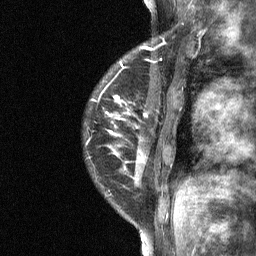
Breast MRI (dynamic contrast-enhanced), one sagittal slice. Slice 16 of 64 in the series (ordered by position). Dynamic contrast-enhanced study with each time point stored as its own series, time point 2 of 3 at this slice position (early post-contrast, ordered by acquisition time). 1.5 T. TE 4.8 ms, TR 27 ms. 2 mm slice thickness. 256 × 256 image matrix, field of view 180 × 180 mm. Patient: female, 34 years. From the clinical record (not read from this slice): setting: breast cancer imaged before/during neoadjuvant chemotherapy; receptor status: HR-positive, HER2-negative.
Outlined on this slice (semi-automatic segmentation, software-assisted and operator-edited):
- analysis volume of interest (the breast-tissue region the enhancement analysis was run in; not a lesion): bounding box <83,44,181,191> (left, top, right, bottom; pixels)
- tumour enhancement mask (voxels above the 90 % enhancement threshold inside the analysis volume of interest): <107,46,158,150>